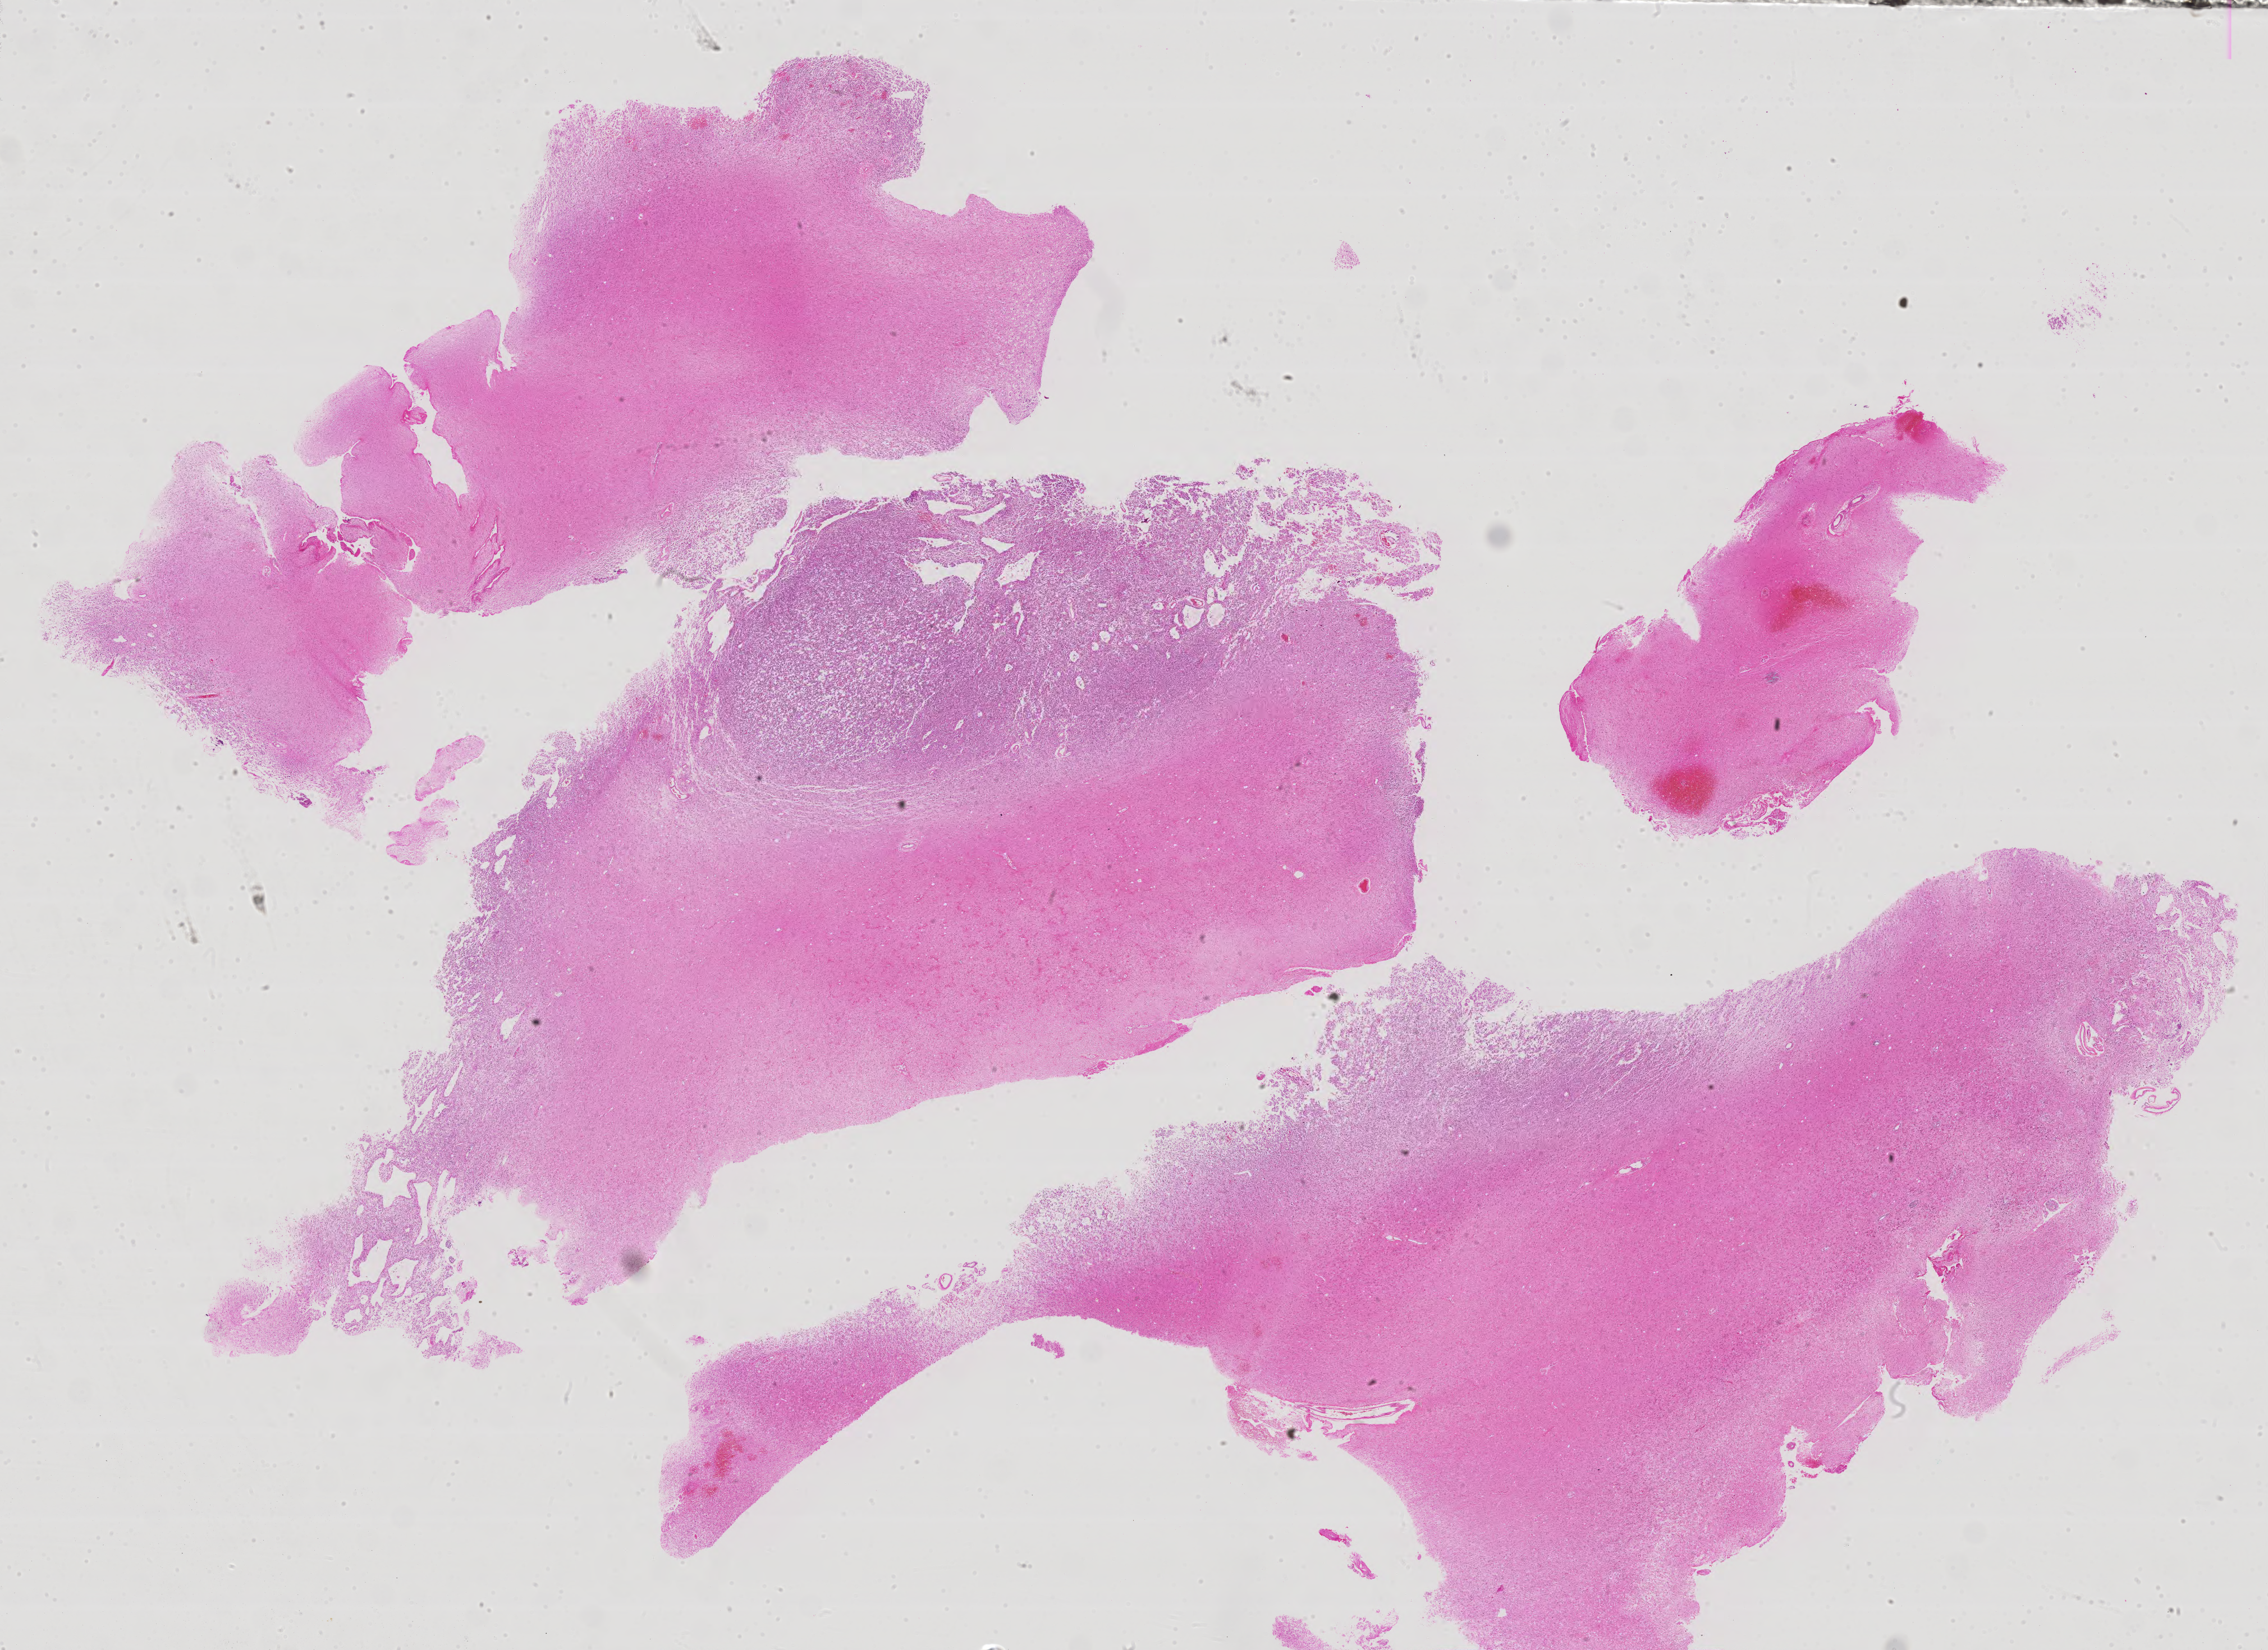
H&E whole-slide image, a low-resolution overview of the entire scanned area, about 32.3 x 23.5 mm; formalin-fixed paraffin-embedded (FFPE) diagnostic section; primary tumour sample from the brain. Male, age 35 years at initial diagnosis. Histologic grade: G2 (moderately differentiated).
Laterality: left. Pathologic diagnosis: Astrocytoma, NOS (cerebrum).